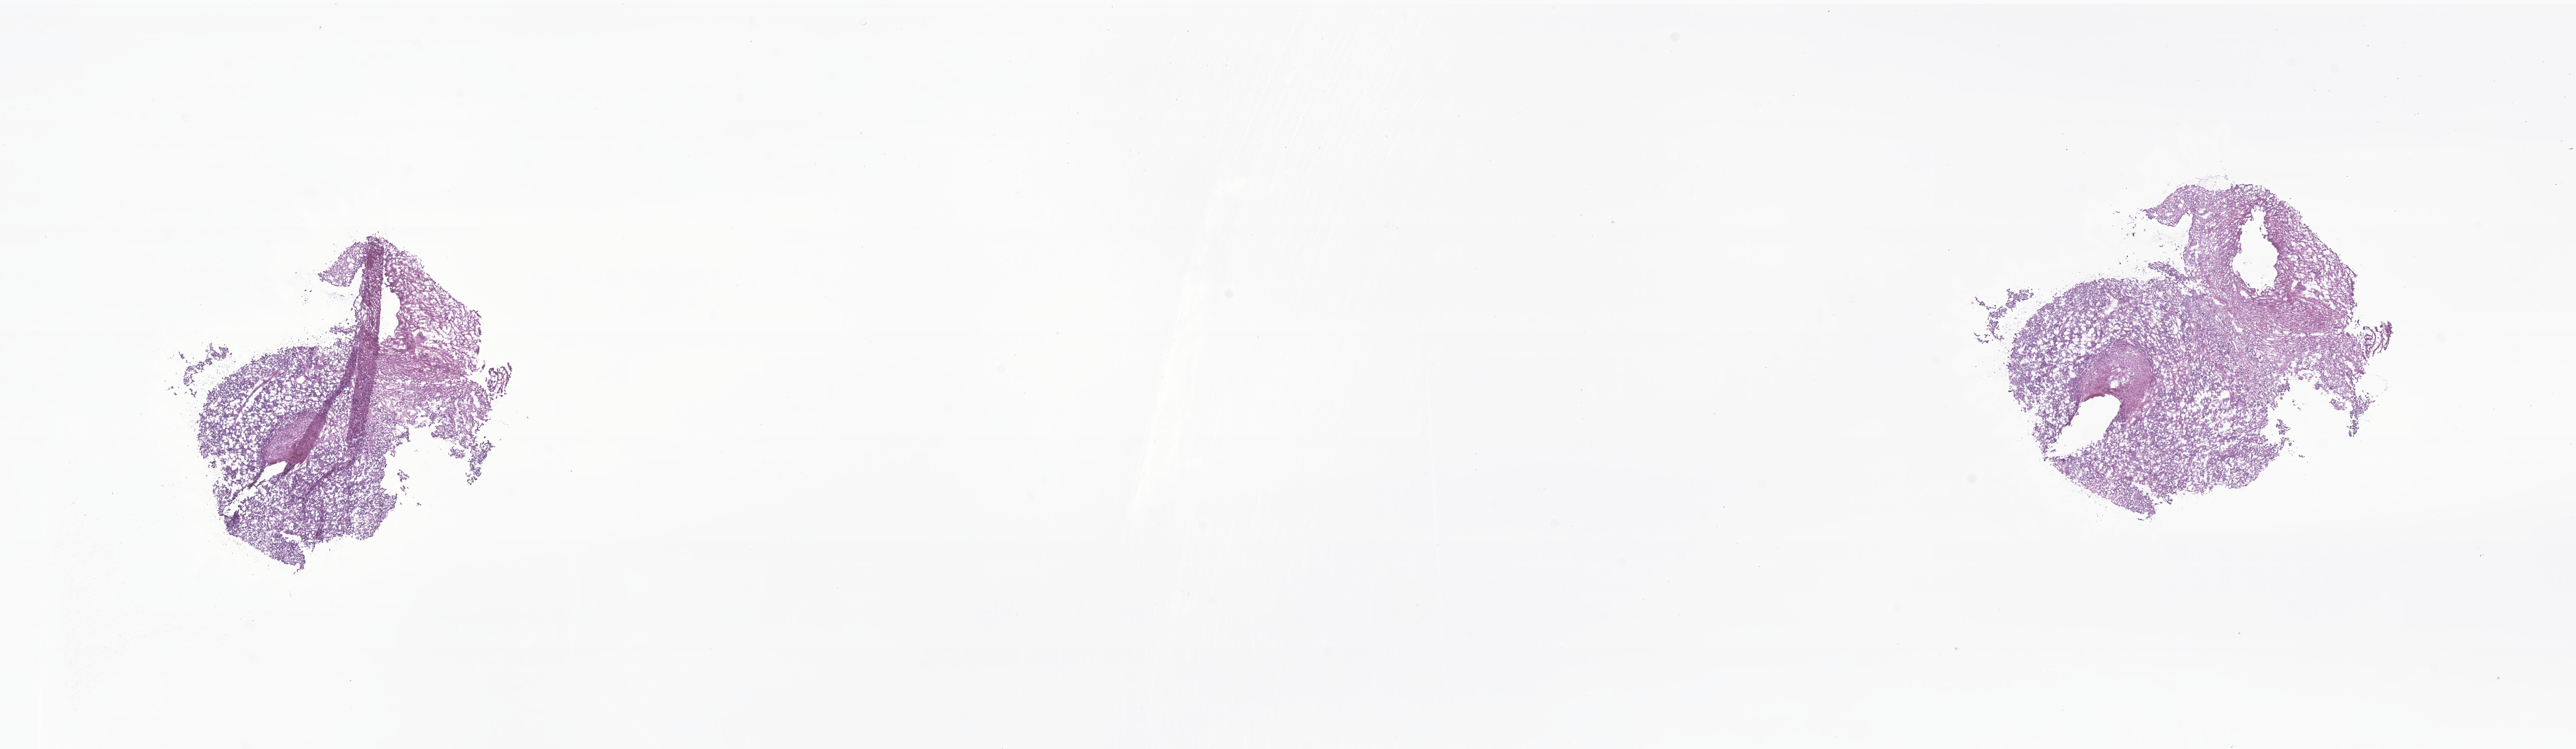
Haematoxylin and eosin whole-slide image of tumor tissue from the brain — shown as a low-resolution overview of the whole scanned area (about 26.1 x 7.6 mm), frozen section. Male patient, age 116 months (9 years 8 months).
Diagnosis (ICD-O-3 morphology term): Ependymoma, NOS.